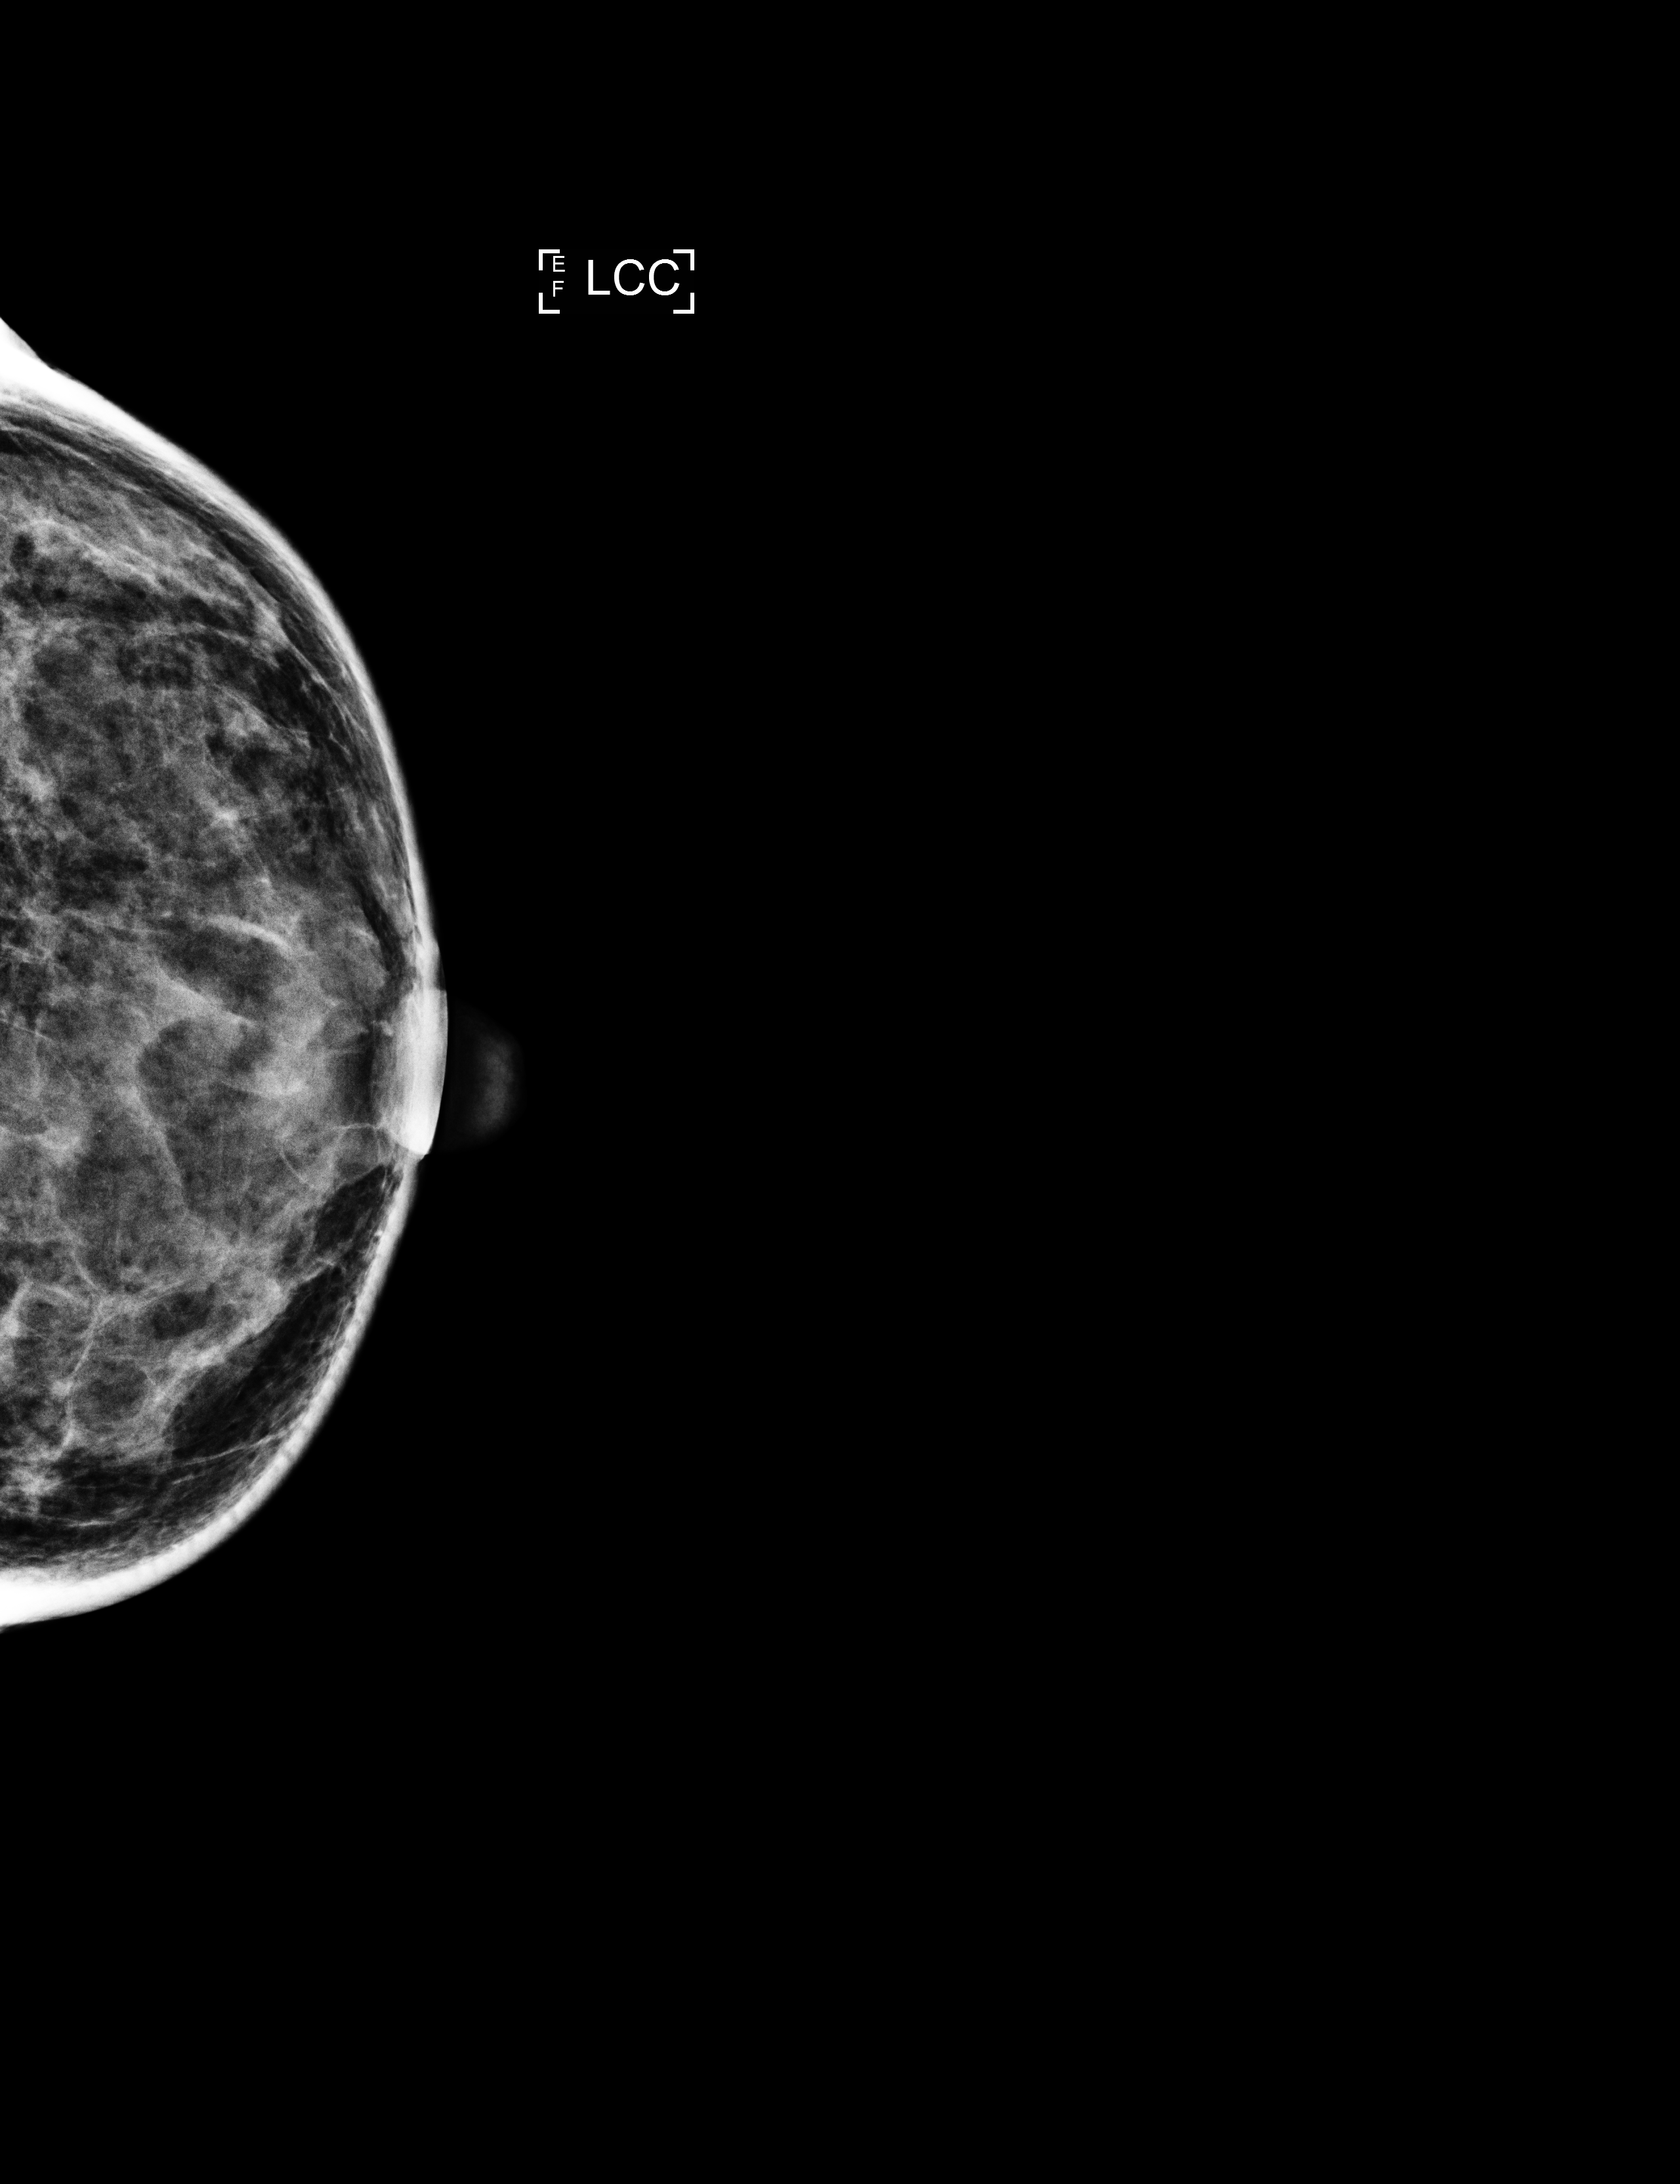
Digital mammogram (FFDM); left breast; cranio-caudal projection; annual screening mammography examination. Patient aged 59 years (female).
Breast density at the screening exam (both breasts): heterogeneously dense (BI-RADS density category c). Final BI-RADS category for the screening round (tomosynthesis exam, both breasts): category 2. Recall: no recall after this screen.